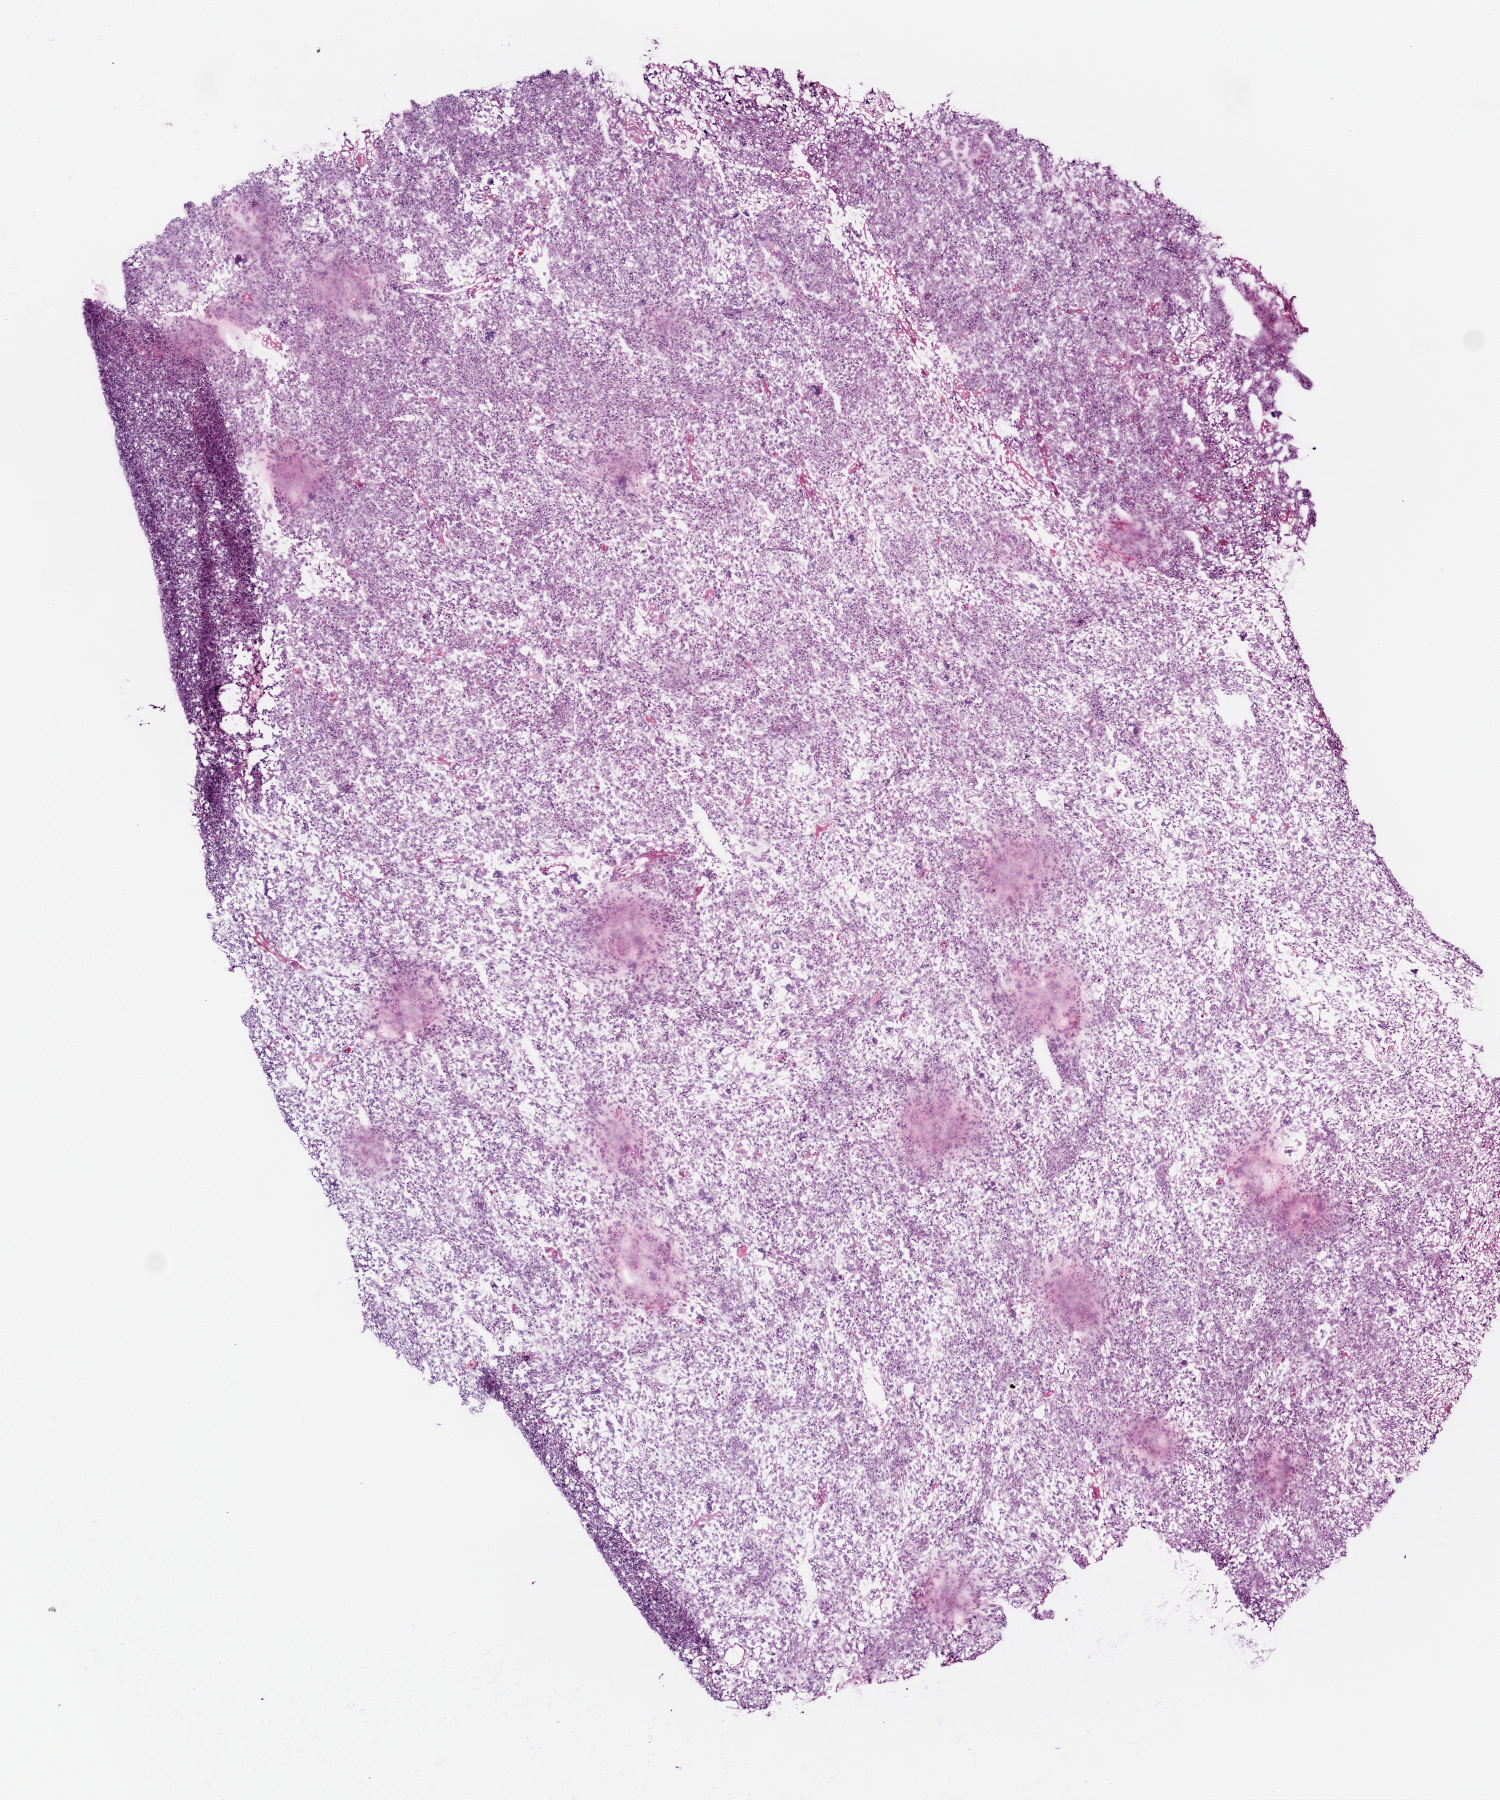
Hematoxylin and eosin (H&E) stained whole-slide image — shown as a low-resolution overview of the whole scanned area (about 6.0 x 7.2 mm, from a 20x scan), frozen section from the top of the tissue portion, primary tumour sample from the brain. Patient: female, age at initial diagnosis 24 years.
Diagnosis: Glioblastoma.